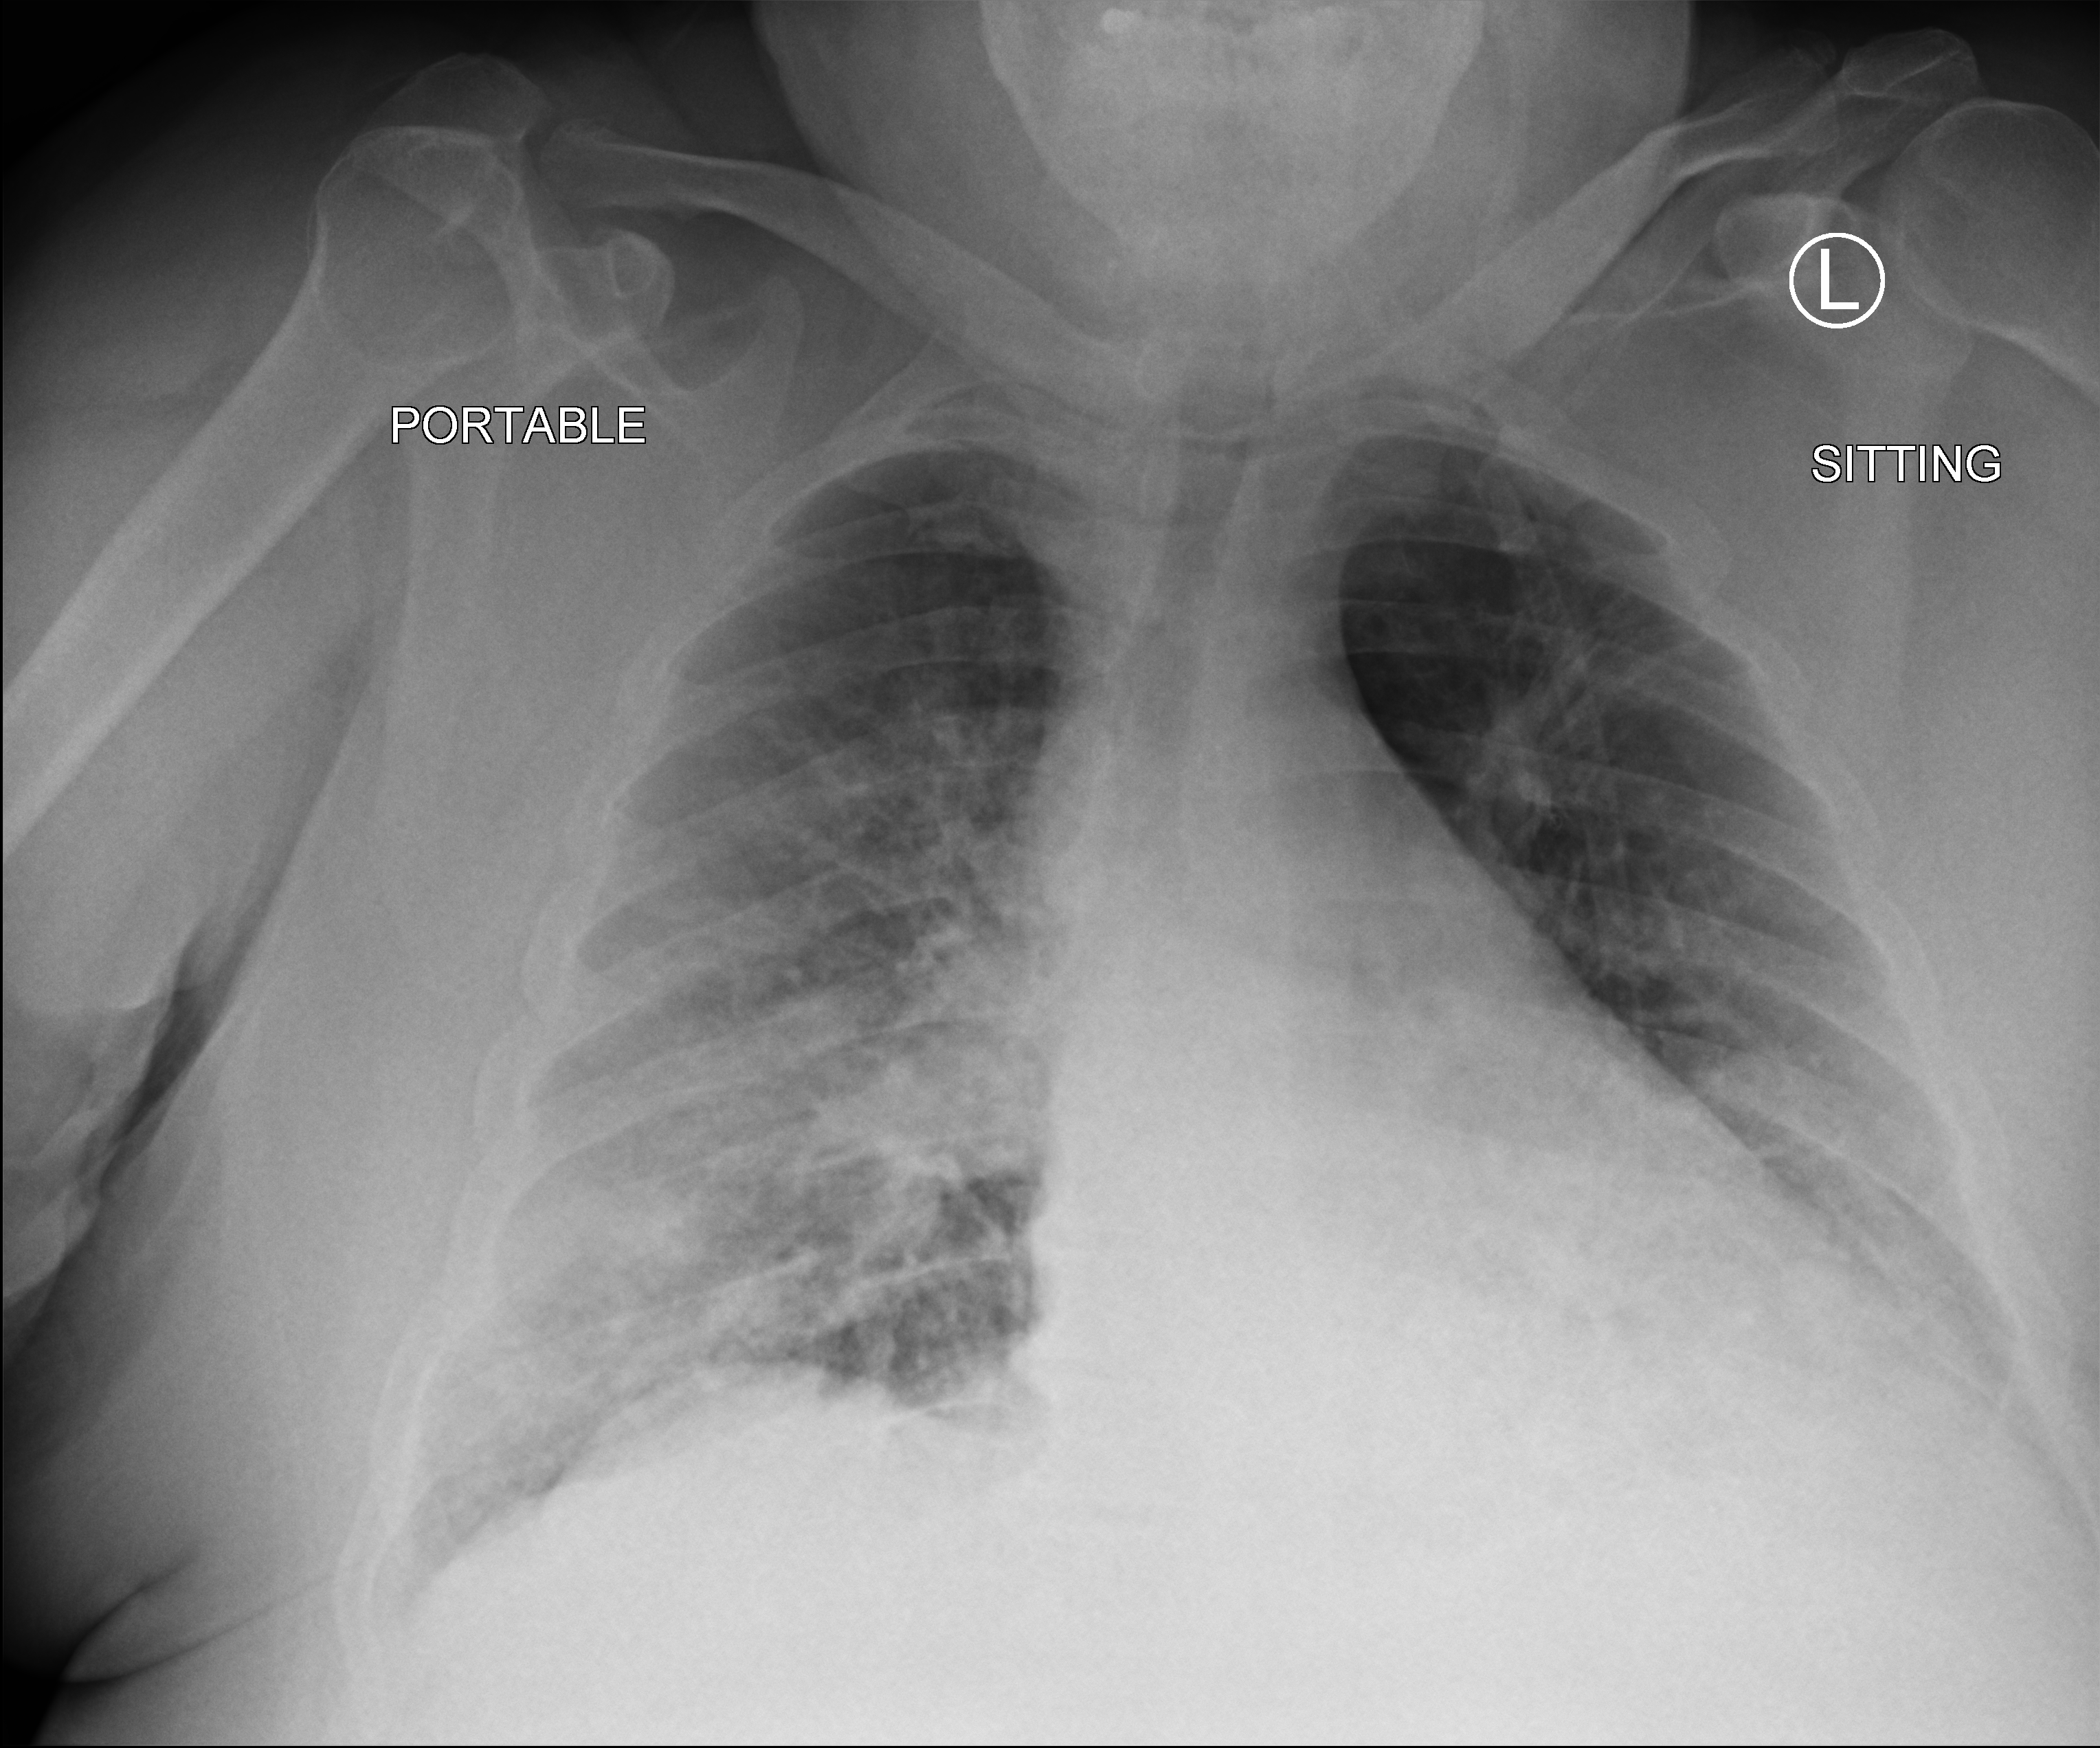
Bedside chest radiograph (computed radiography), anteroposterior (AP) projection. Male patient hospitalised with COVID-19, age 60–74 years.
Admission-level facts for this patient (not findings on this image; timing relative to this image not recorded):
- length of hospital stay: 11 days
- mechanically ventilated during this hospital stay: no
- admitted to intensive care during this hospital stay: yes